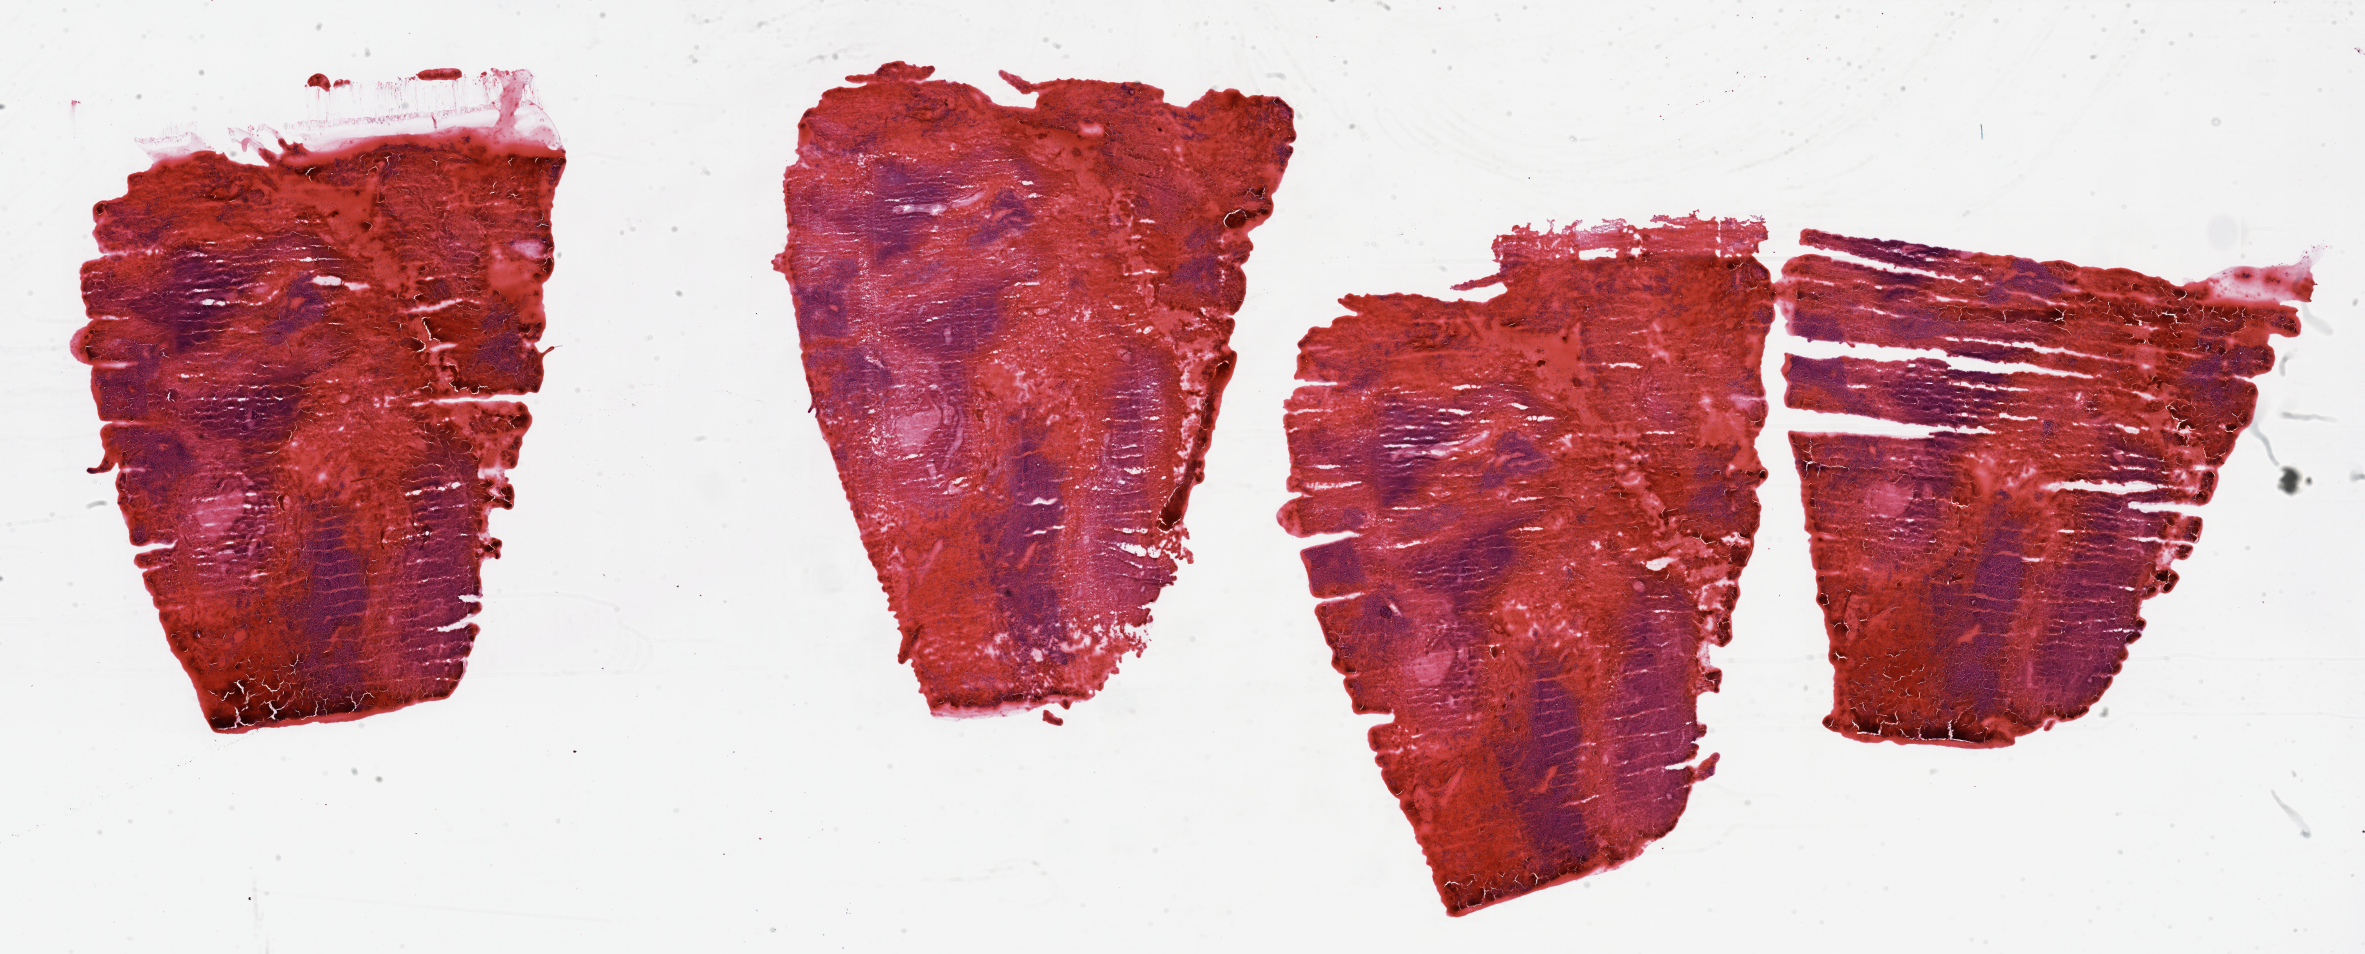
Whole-slide histology image, H&E — whole scanned area (about 37.4 x 15.1 mm) shown as a low-resolution overview. Kidney, tumour tissue. 68-year-old male patient. Histologic grade: G3 (poorly differentiated).
Primary tumour site (as recorded): lower pole. Histologic diagnosis: Renal cell carcinoma, NOS. AJCC pathologic stage: I.